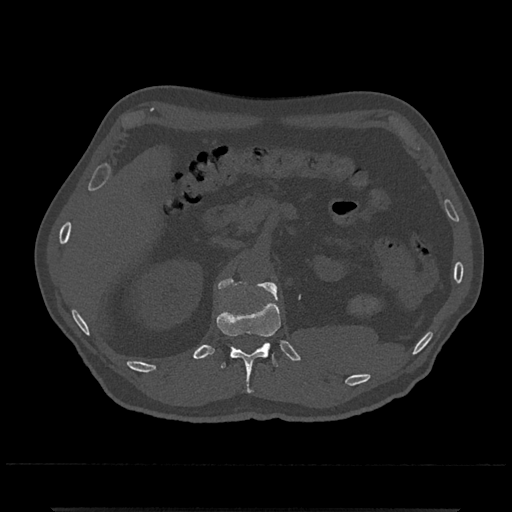
CT including the spine, one axial slice; slice 415 of 797 in the series (ordered by position); reconstruction kernel Br40s/3; bone window (W 1800 / L 400 HU); 0.5 mm slice thickness; 512 × 512 image matrix, field of view 393 × 393 mm. Male patient, age 67 years. From the clinical record (not read from this slice): primary cancer: prostate.
Annotated regions visible in this slice (semi-automatic segmentation, software-assisted and operator-edited):
- L1 vertebra: bounding box [x1, y1, x2, y2] px = [218, 278, 278, 300]
- T12 vertebra: [217, 292, 281, 393]